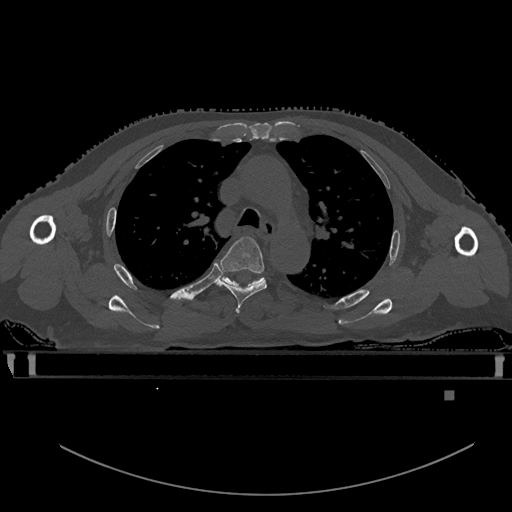
CT including the spine, one axial slice. Slice 395 of 969 in the series (ordered by position). Bone window (W 1800 / L 400 HU). 0.5 mm slice thickness. 512 × 512 image matrix, field of view 456 × 456 mm. Patient: male, 82 years. Case-level facts recorded for this patient, not image findings: primary cancer: prostate; vertebrae with lytic lesions (as recorded): T11, T9, T8, T2.
Structures marked on this image (semi-automatic segmentation, software-assisted and operator-edited):
- T3 vertebra: bounding box [x1, y1, x2, y2] px = [236, 311, 240, 313]
- T4 vertebra: [216, 236, 268, 312]
- T5 vertebra: [219, 272, 265, 286]